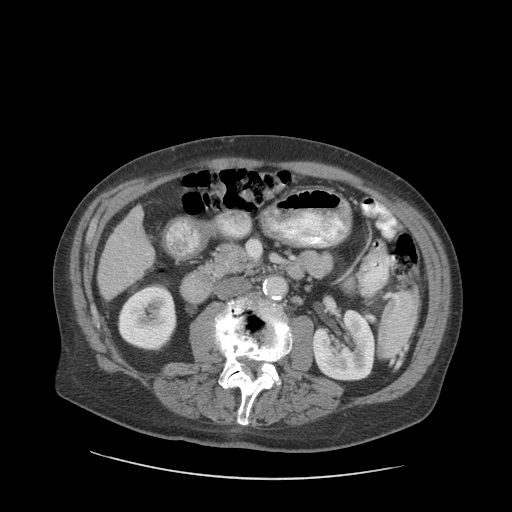
Contrast-enhanced abdominal CT (liver protocol), one axial slice. Slice 30 of 89 in the series (ordered by position). Reconstruction kernel STANDARD. 140 kVp. Soft-tissue window (W 400 / L 40 HU). 2.5 mm slice thickness. 512 × 512 image matrix, field of view 420 × 420 mm. From the clinical record (not read from this slice): diagnosis: hepatocellular carcinoma (patient treated with transarterial chemoembolisation; whether this scan precedes or follows treatment is not stated here); TNM stage (as recorded): Stage-I; Child-Pugh class: A; tumour size: 4.6 cm.
Annotated regions visible in this slice (semi-automatic segmentation, software-assisted and operator-edited):
- liver parenchyma outside the tumour (the mass and vessels are separate outlines, so this box may not span the whole liver): bounding box (x1, y1, x2, y2) in pixels: (98, 206, 154, 300)
- liver vessels: (127, 244, 149, 274)